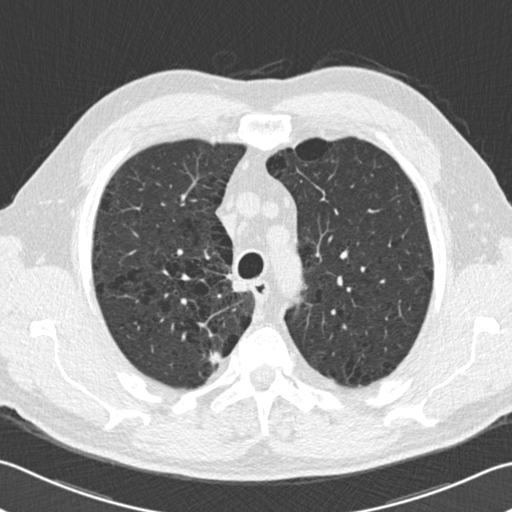
Chest CT (low-dose screening protocol), one axial image, second annual screen, lung window (W 1500 / L -600 HU), 2 mm slice thickness, 120 kVp. Male participant, aged 68 years at enrolment.
Expert reader's lesion annotation, bounding box <197,341,232,374> (left, top, right, bottom; pixels). The exam's reader record, not a measurement of the box and not confirmed to be the same lesion: non-calcified nodule or mass ≥4 mm, right upper lobe, 30 × 20 mm, smooth margins, pre-existing on the prior screen: no.